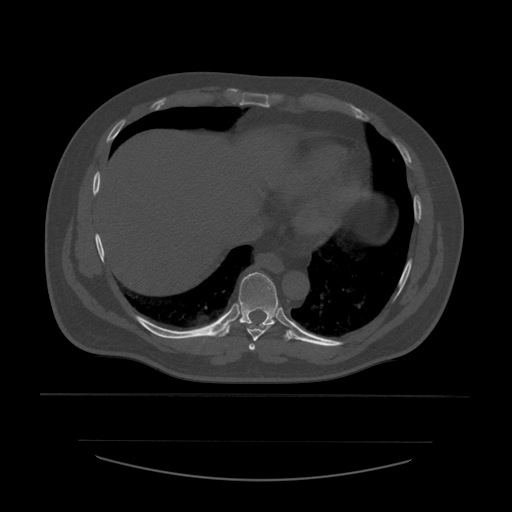
CT including the spine, one axial slice. Slice 326 of 532 in the series (ordered by position). 120 kVp. Bone window (W 1800 / L 400 HU). 1.25 mm slice thickness. 512 × 512 image matrix, field of view 441 × 441 mm. Patient age 44 years. Case-level facts recorded for this patient, not image findings: primary cancer: soft tissue sarcoma.
Annotated regions visible in this slice (semi-automatic segmentation, software-assisted and operator-edited):
- T7 vertebra: box from (x=249, y=344) to (x=256, y=352) px
- T8 vertebra: (x=247, y=323)–(x=272, y=342)
- T9 vertebra: (x=216, y=272)–(x=293, y=341)